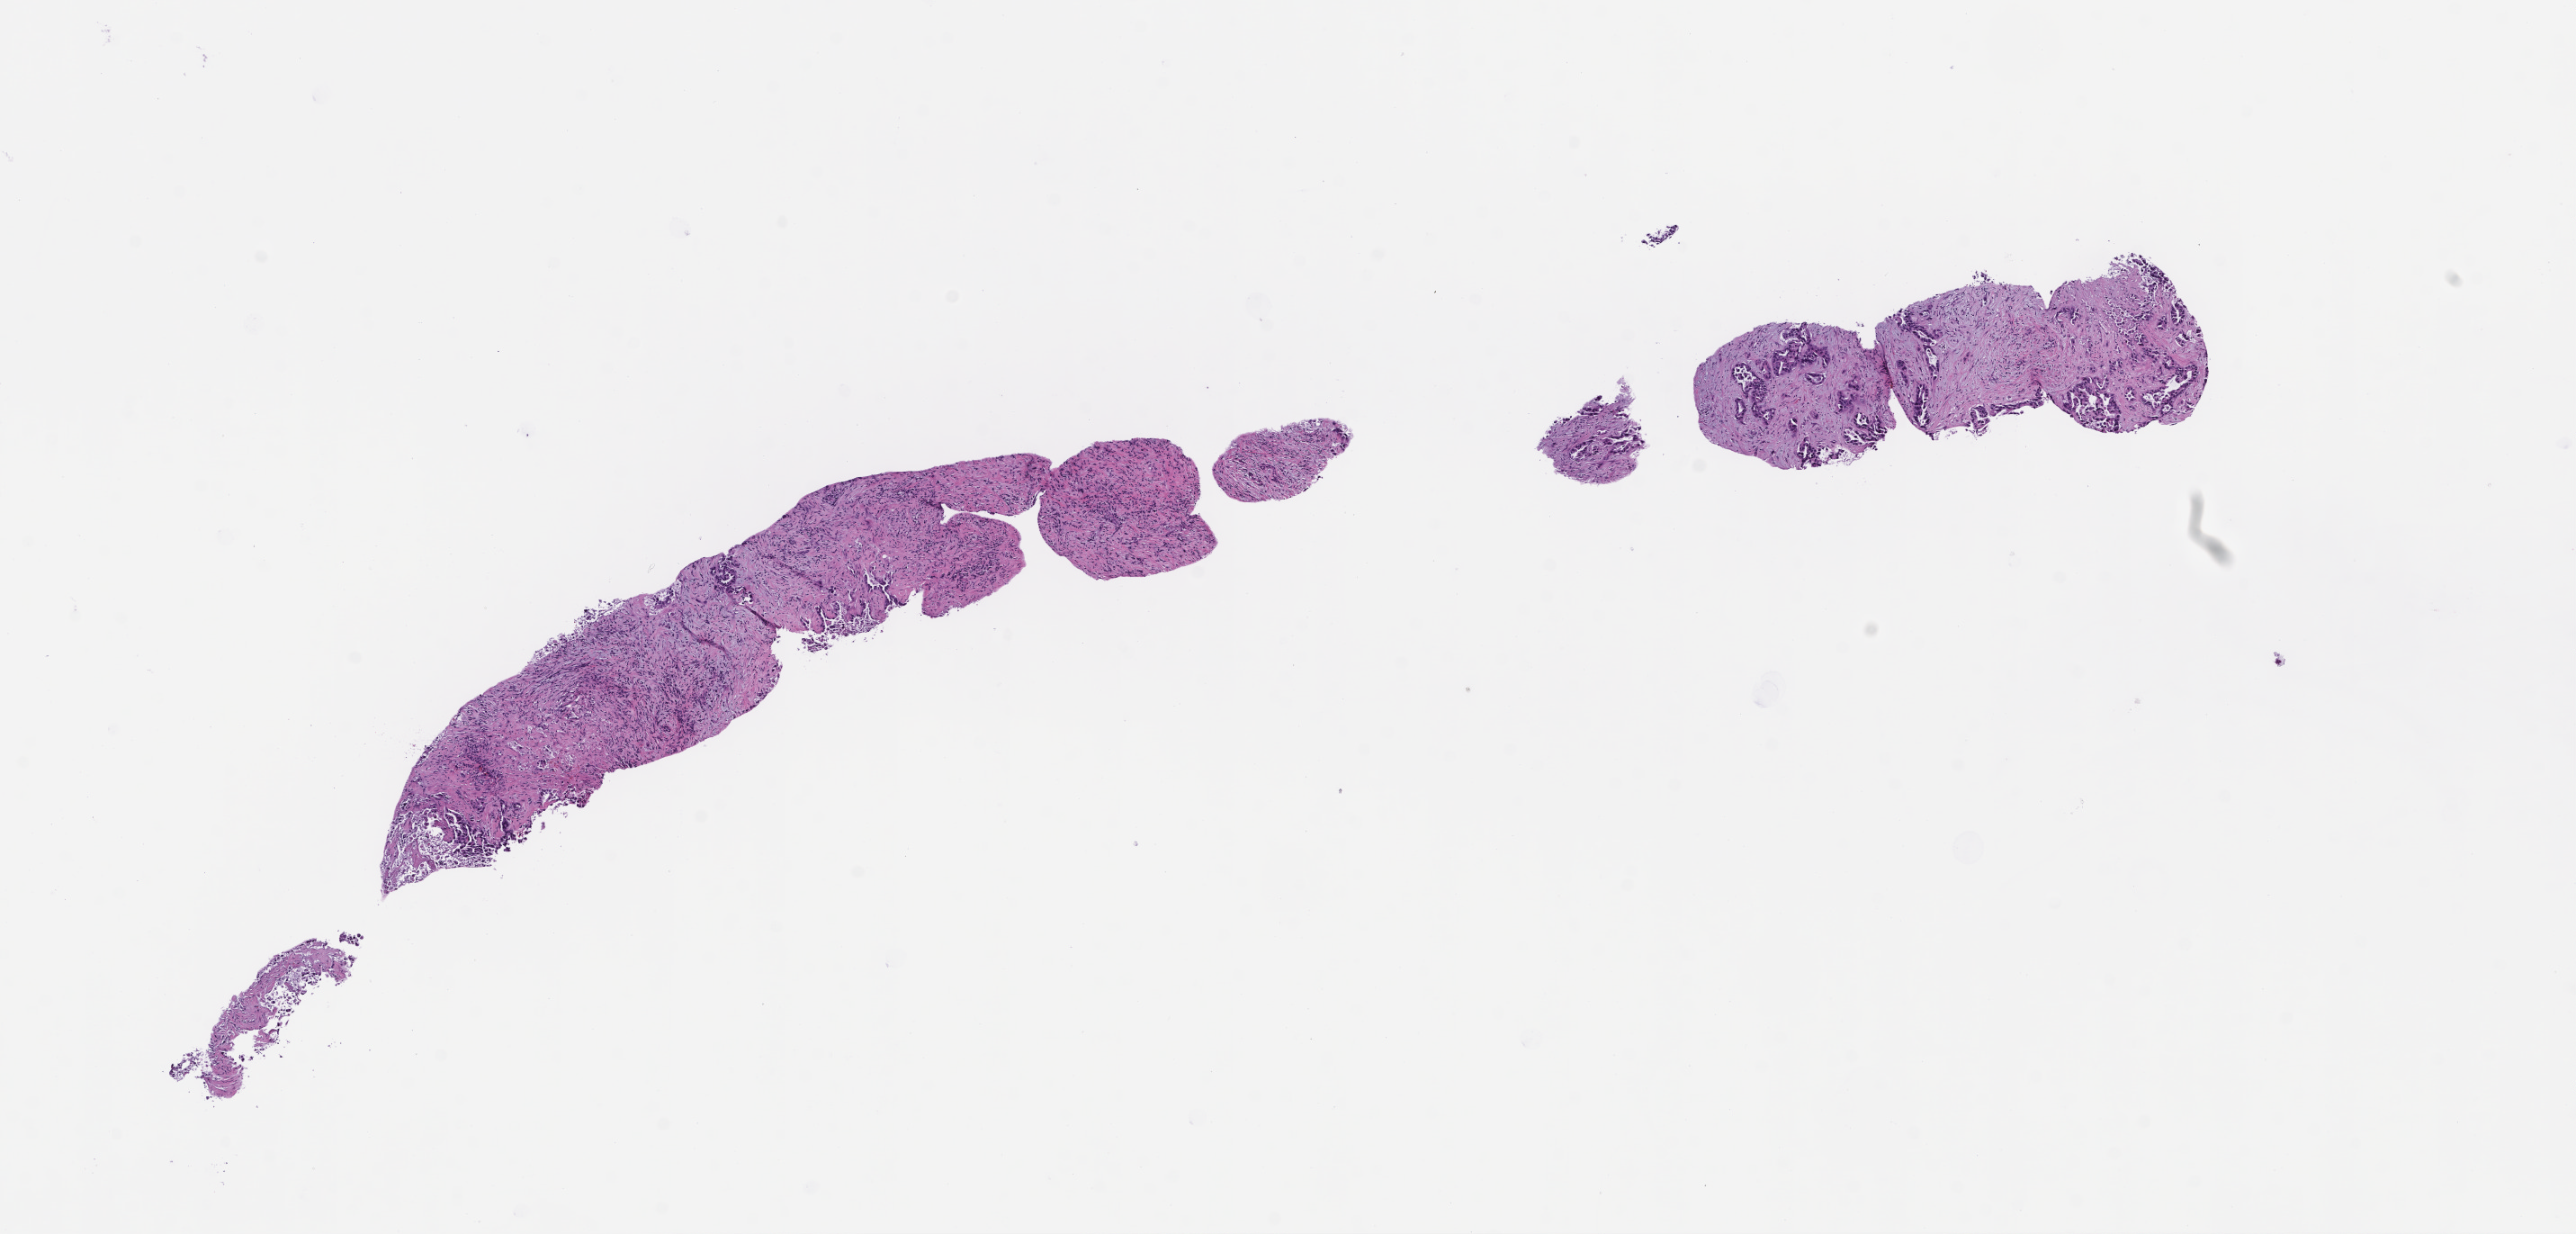
Haematoxylin and eosin whole-slide image — a low-resolution overview of the entire scanned area, about 11.6 x 5.5 mm, formalin-fixed, paraffin-embedded (FFPE) tissue, specimen time point: collected at baseline (before treatment). Female patient.
This section: metastatic tumor tissue. Patient diagnosis (primary): Non-Small Cell Lung Carcinoma.